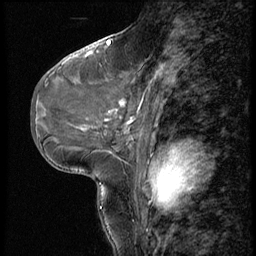
Breast MRI (dynamic contrast-enhanced), one sagittal slice. Slice 28 of 56 in the series (ordered by position). 3 images stored at this slice position (order not interpretable as contrast timing). 1.5 T. TE 4.2 ms, TR 9 ms. 2.5 mm slice thickness. 256 × 256 image matrix. Patient: female, 46 years. Case-level facts recorded for this patient, not image findings: setting: breast cancer imaged before/during neoadjuvant chemotherapy; receptor status: HER2-positive.
Outlined on this slice (semi-automatic segmentation, software-assisted and operator-edited):
- analysis volume of interest (the breast-tissue region the enhancement analysis was run in; not a lesion): bounding box [x1, y1, x2, y2] px = [79, 68, 184, 143]
- tumour enhancement mask (voxels above the 140 % enhancement threshold inside the analysis volume of interest): [125, 131, 127, 133]